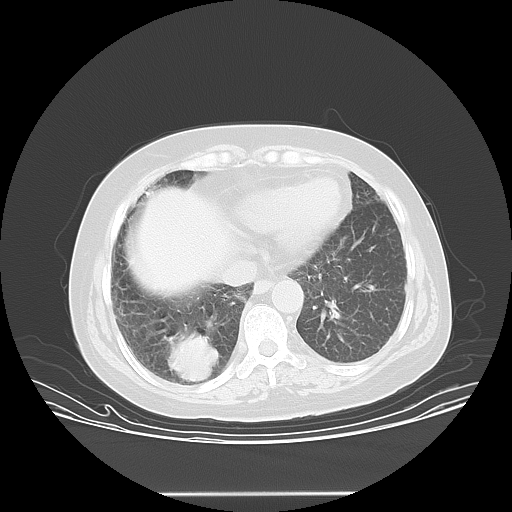
Chest CT, one axial slice. Position 10 of 45 along the scan axis. Reconstruction kernel LUNG. 120 kVp. Lung window (W 1500 / L -600 HU). 512 × 512 image matrix. Female patient, age 55 years. Case-level facts recorded for this patient, not image findings: clinical TNM (as recorded): T2 N0 M1b.
Outlined on this slice (rectangle marked by the reading radiologist):
- lung tumour (recorded histology: squamous cell carcinoma): box from (x=163, y=322) to (x=226, y=392) px